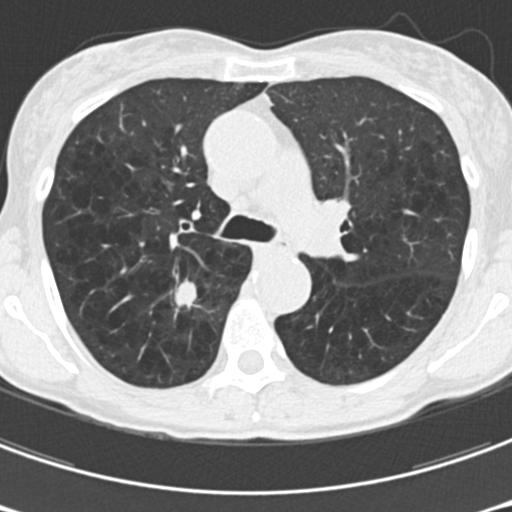
Axial slice from a low-dose chest CT screening exam; third annual screen; lung window (W 1500 / L -600 HU); 2 mm slice thickness; standard (soft-tissue) reconstruction kernel (B30f); slice 64 of 176 in the series; 512 × 512 image matrix. Female, age 61 years at enrolment.
• Expert-annotated lung lesion, box from (x=162, y=268) to (x=223, y=327) px.
• The screening reader recorded 2 non-calcified nodules or masses ≥4 mm on this exam; which of them this box marks is not recorded.
• Official screen result: positive, other.
• Participant outcome: lung cancer diagnosed 77 days after this screen — non-small cell carcinoma, right upper lobe, undifferentiated (G4), stage IA (AJCC 6th edition), 15 mm at pathology.